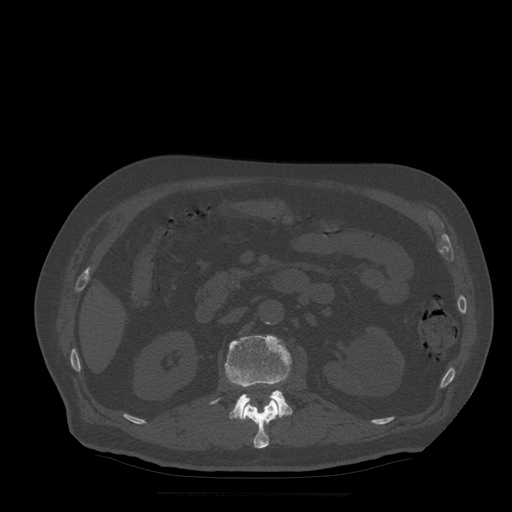
CT including the spine, one axial slice; position 181 of 522 along the scan axis; bone window (W 1800 / L 400 HU); 1.25 mm slice thickness; 512 × 512 image matrix, field of view 420 × 420 mm. Patient age 72 years. Case-level facts recorded for this patient, not image findings: primary cancer: prostate.
Outlined on this slice (semi-automatically segmented with operator editing):
- L1 vertebra: bounding box [x1, y1, x2, y2] px = [242, 383, 280, 449]
- L2 vertebra: [211, 335, 293, 420]